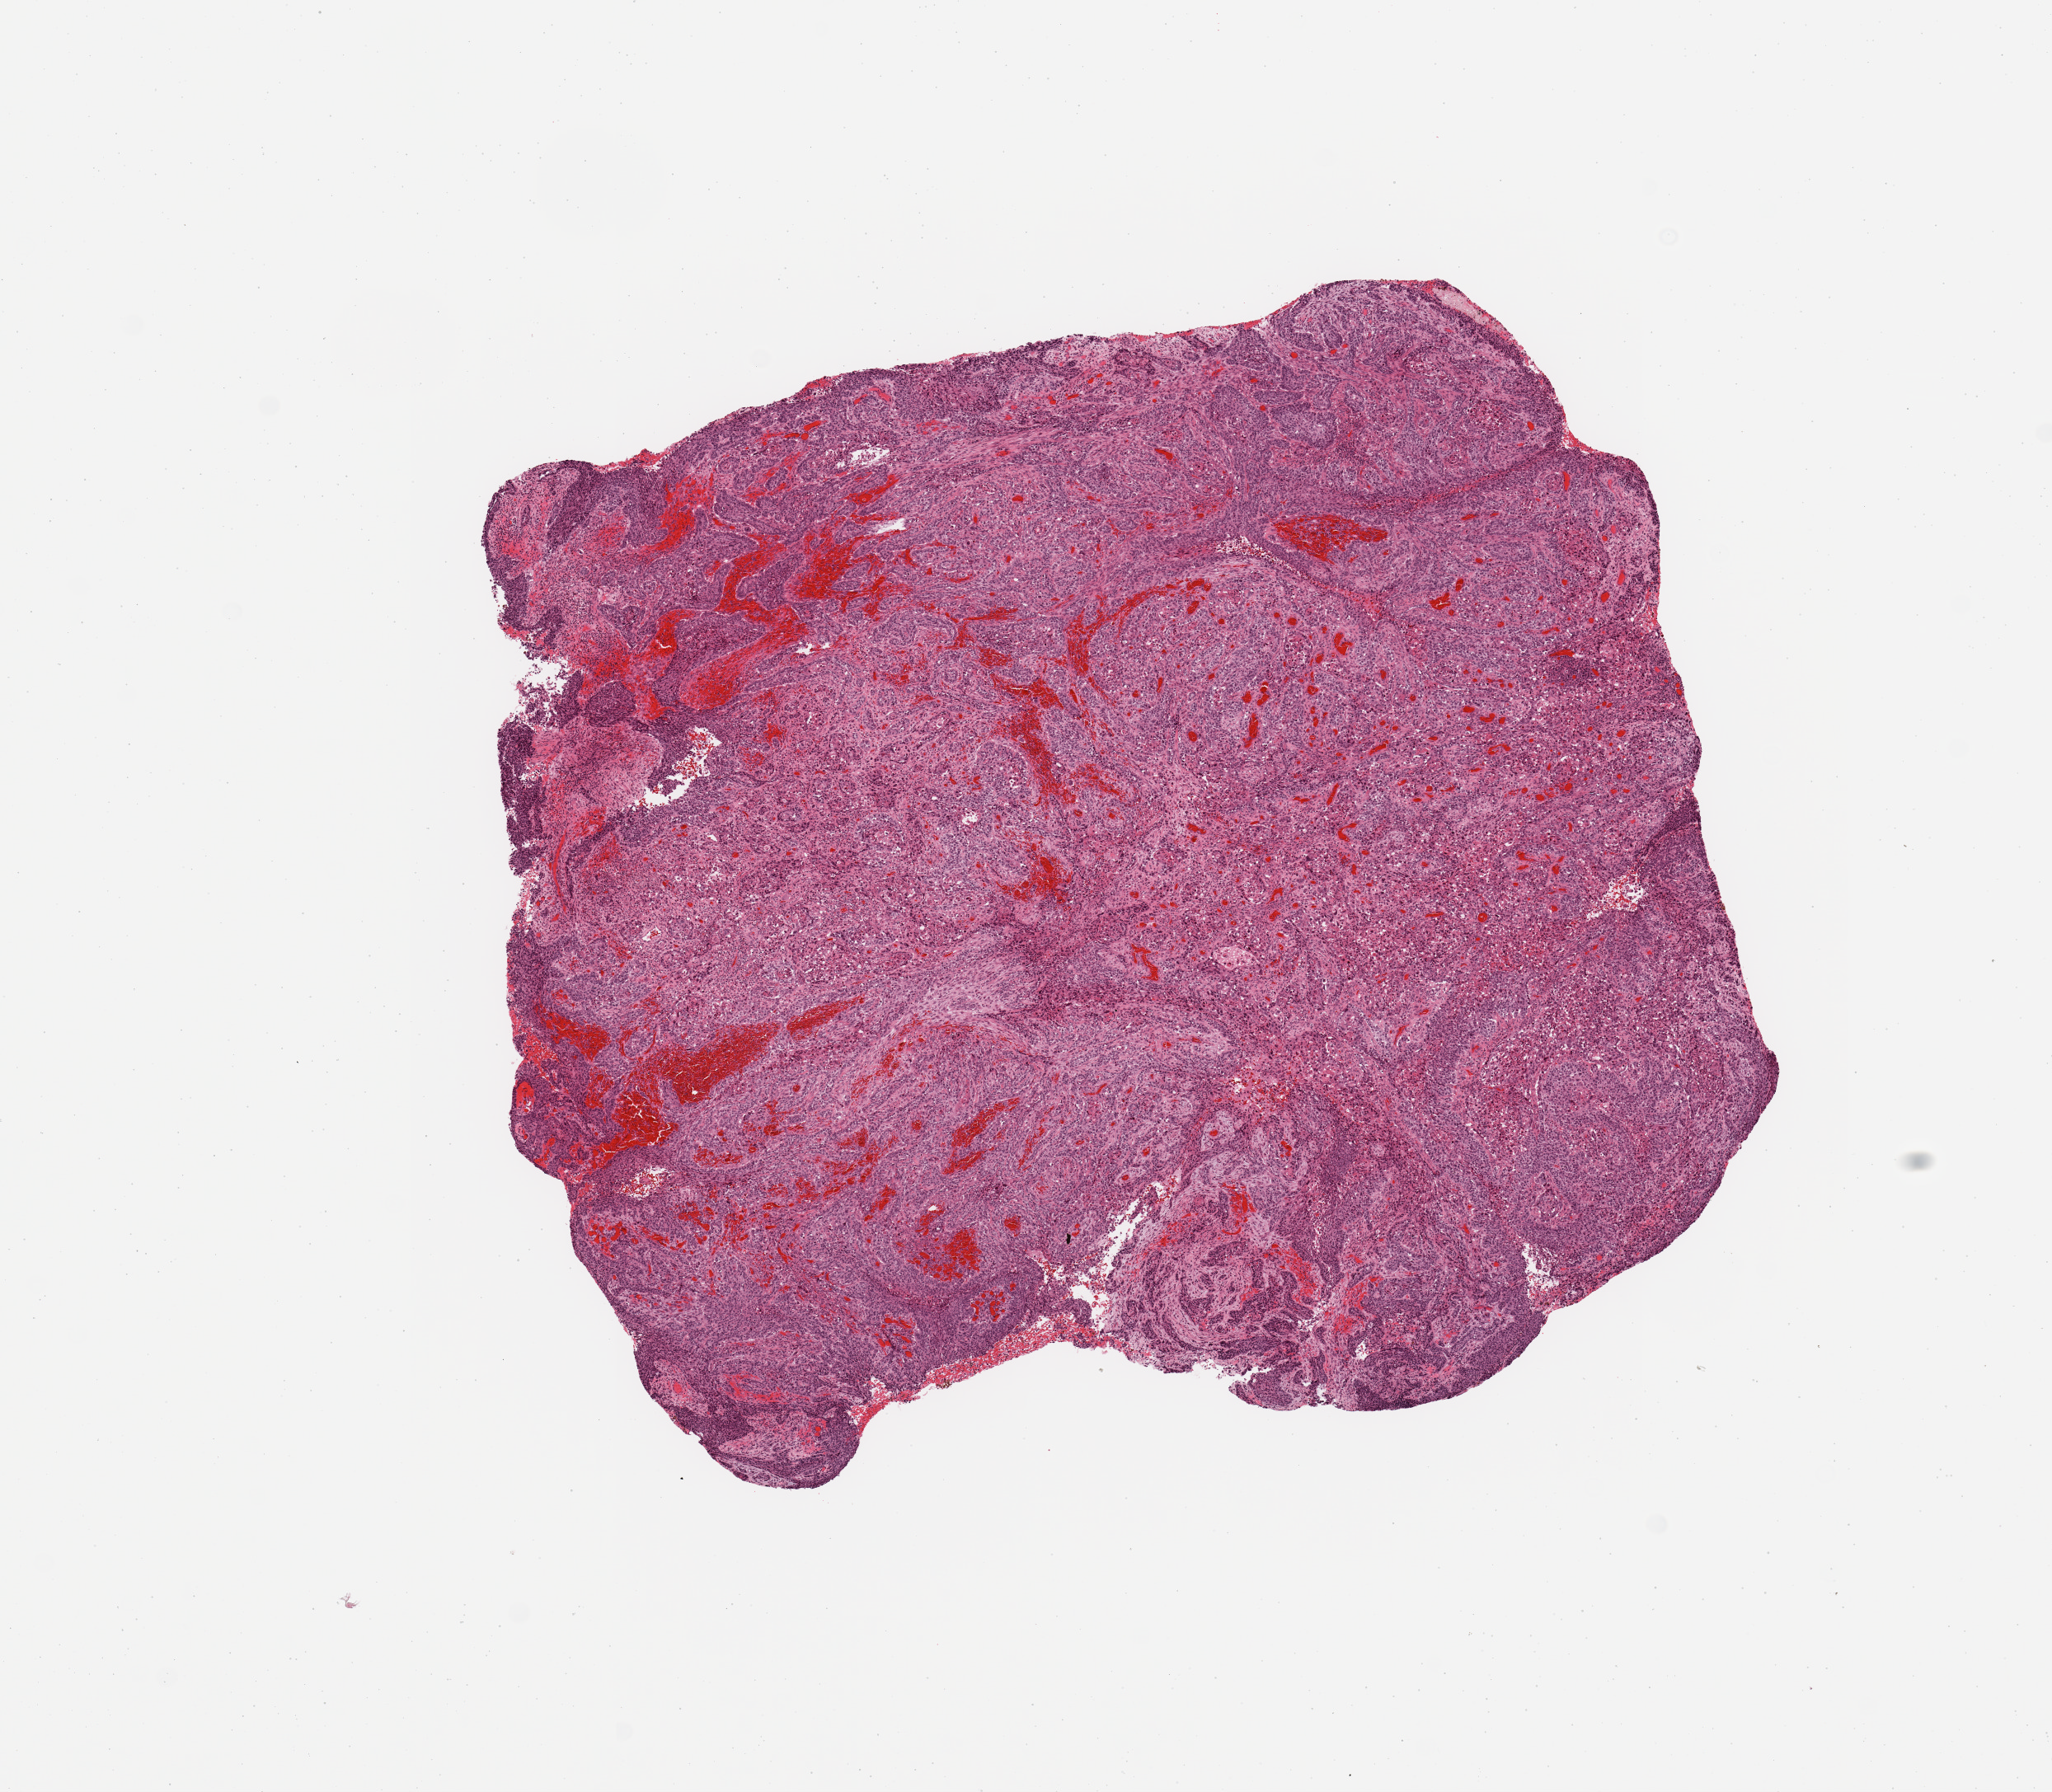
Whole-slide histology image, H&E, low-resolution overview of the scanned area, about 9.8 x 8.6 mm (acquisition: 20x scan). Tumour tissue sample, lung. Patient: male, age 74 years. Histologic grade: G2 (moderately differentiated).
Primary tumour site (as recorded): left lower lobe. AJCC pathologic stage: IIIA. Diagnosis: Squamous cell carcinoma, NOS.